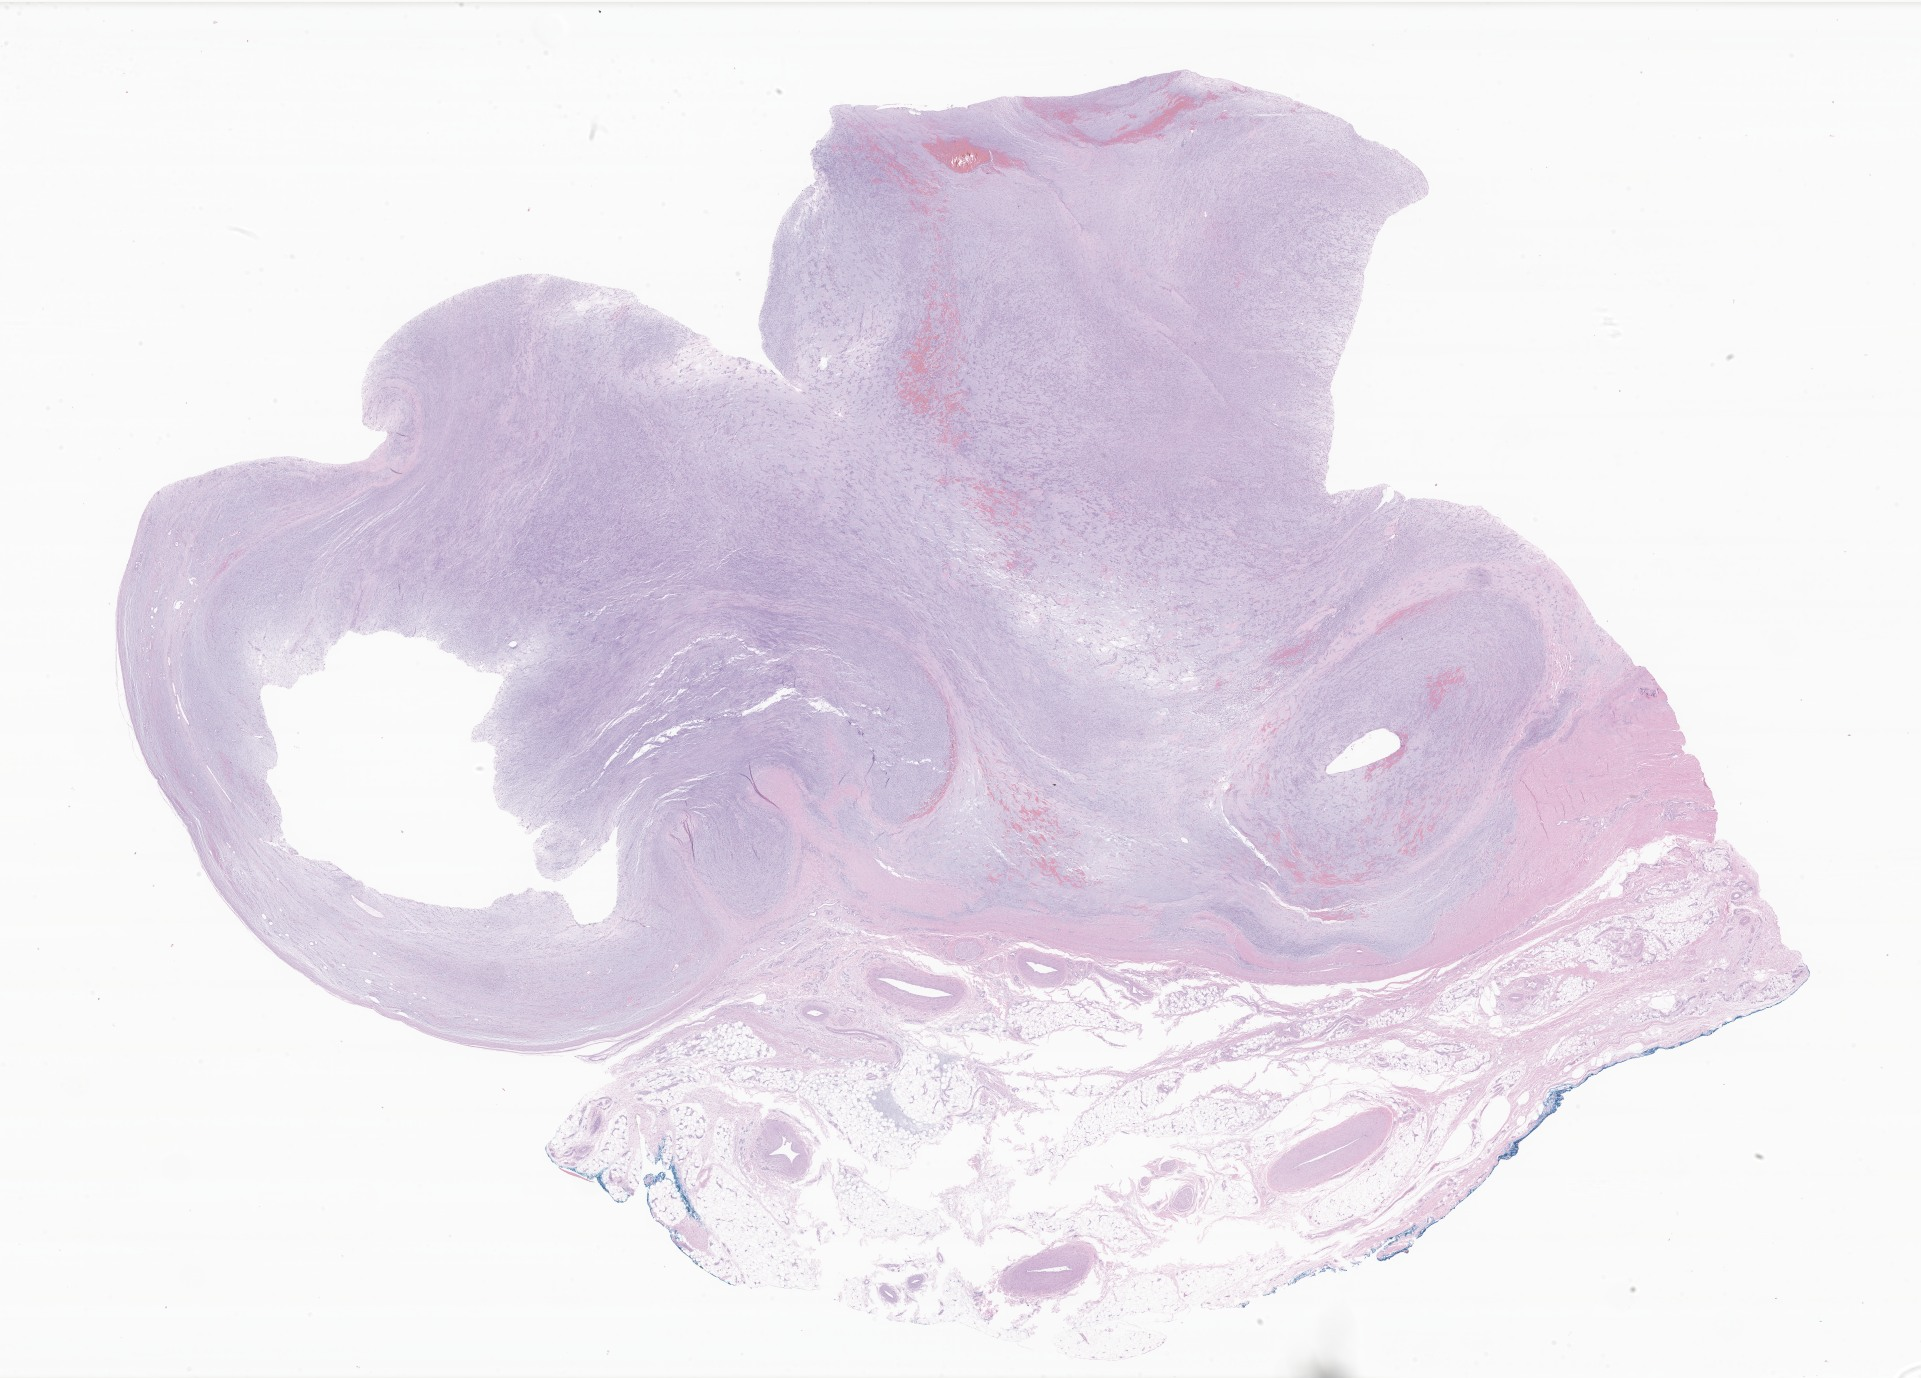
Digitized haematoxylin and eosin-stained section of tumor tissue from the soft tissue of lower extremity — a low-resolution overview of the entire scanned area, about 32.4 x 23.2 mm, formalin-fixed paraffin-embedded section. Patient male; age 171 months.
Tissue or organ of origin (case record): connective, subcutaneous and other soft tissues of lower limb and hip. Diagnosis: Undifferentiated sarcoma.